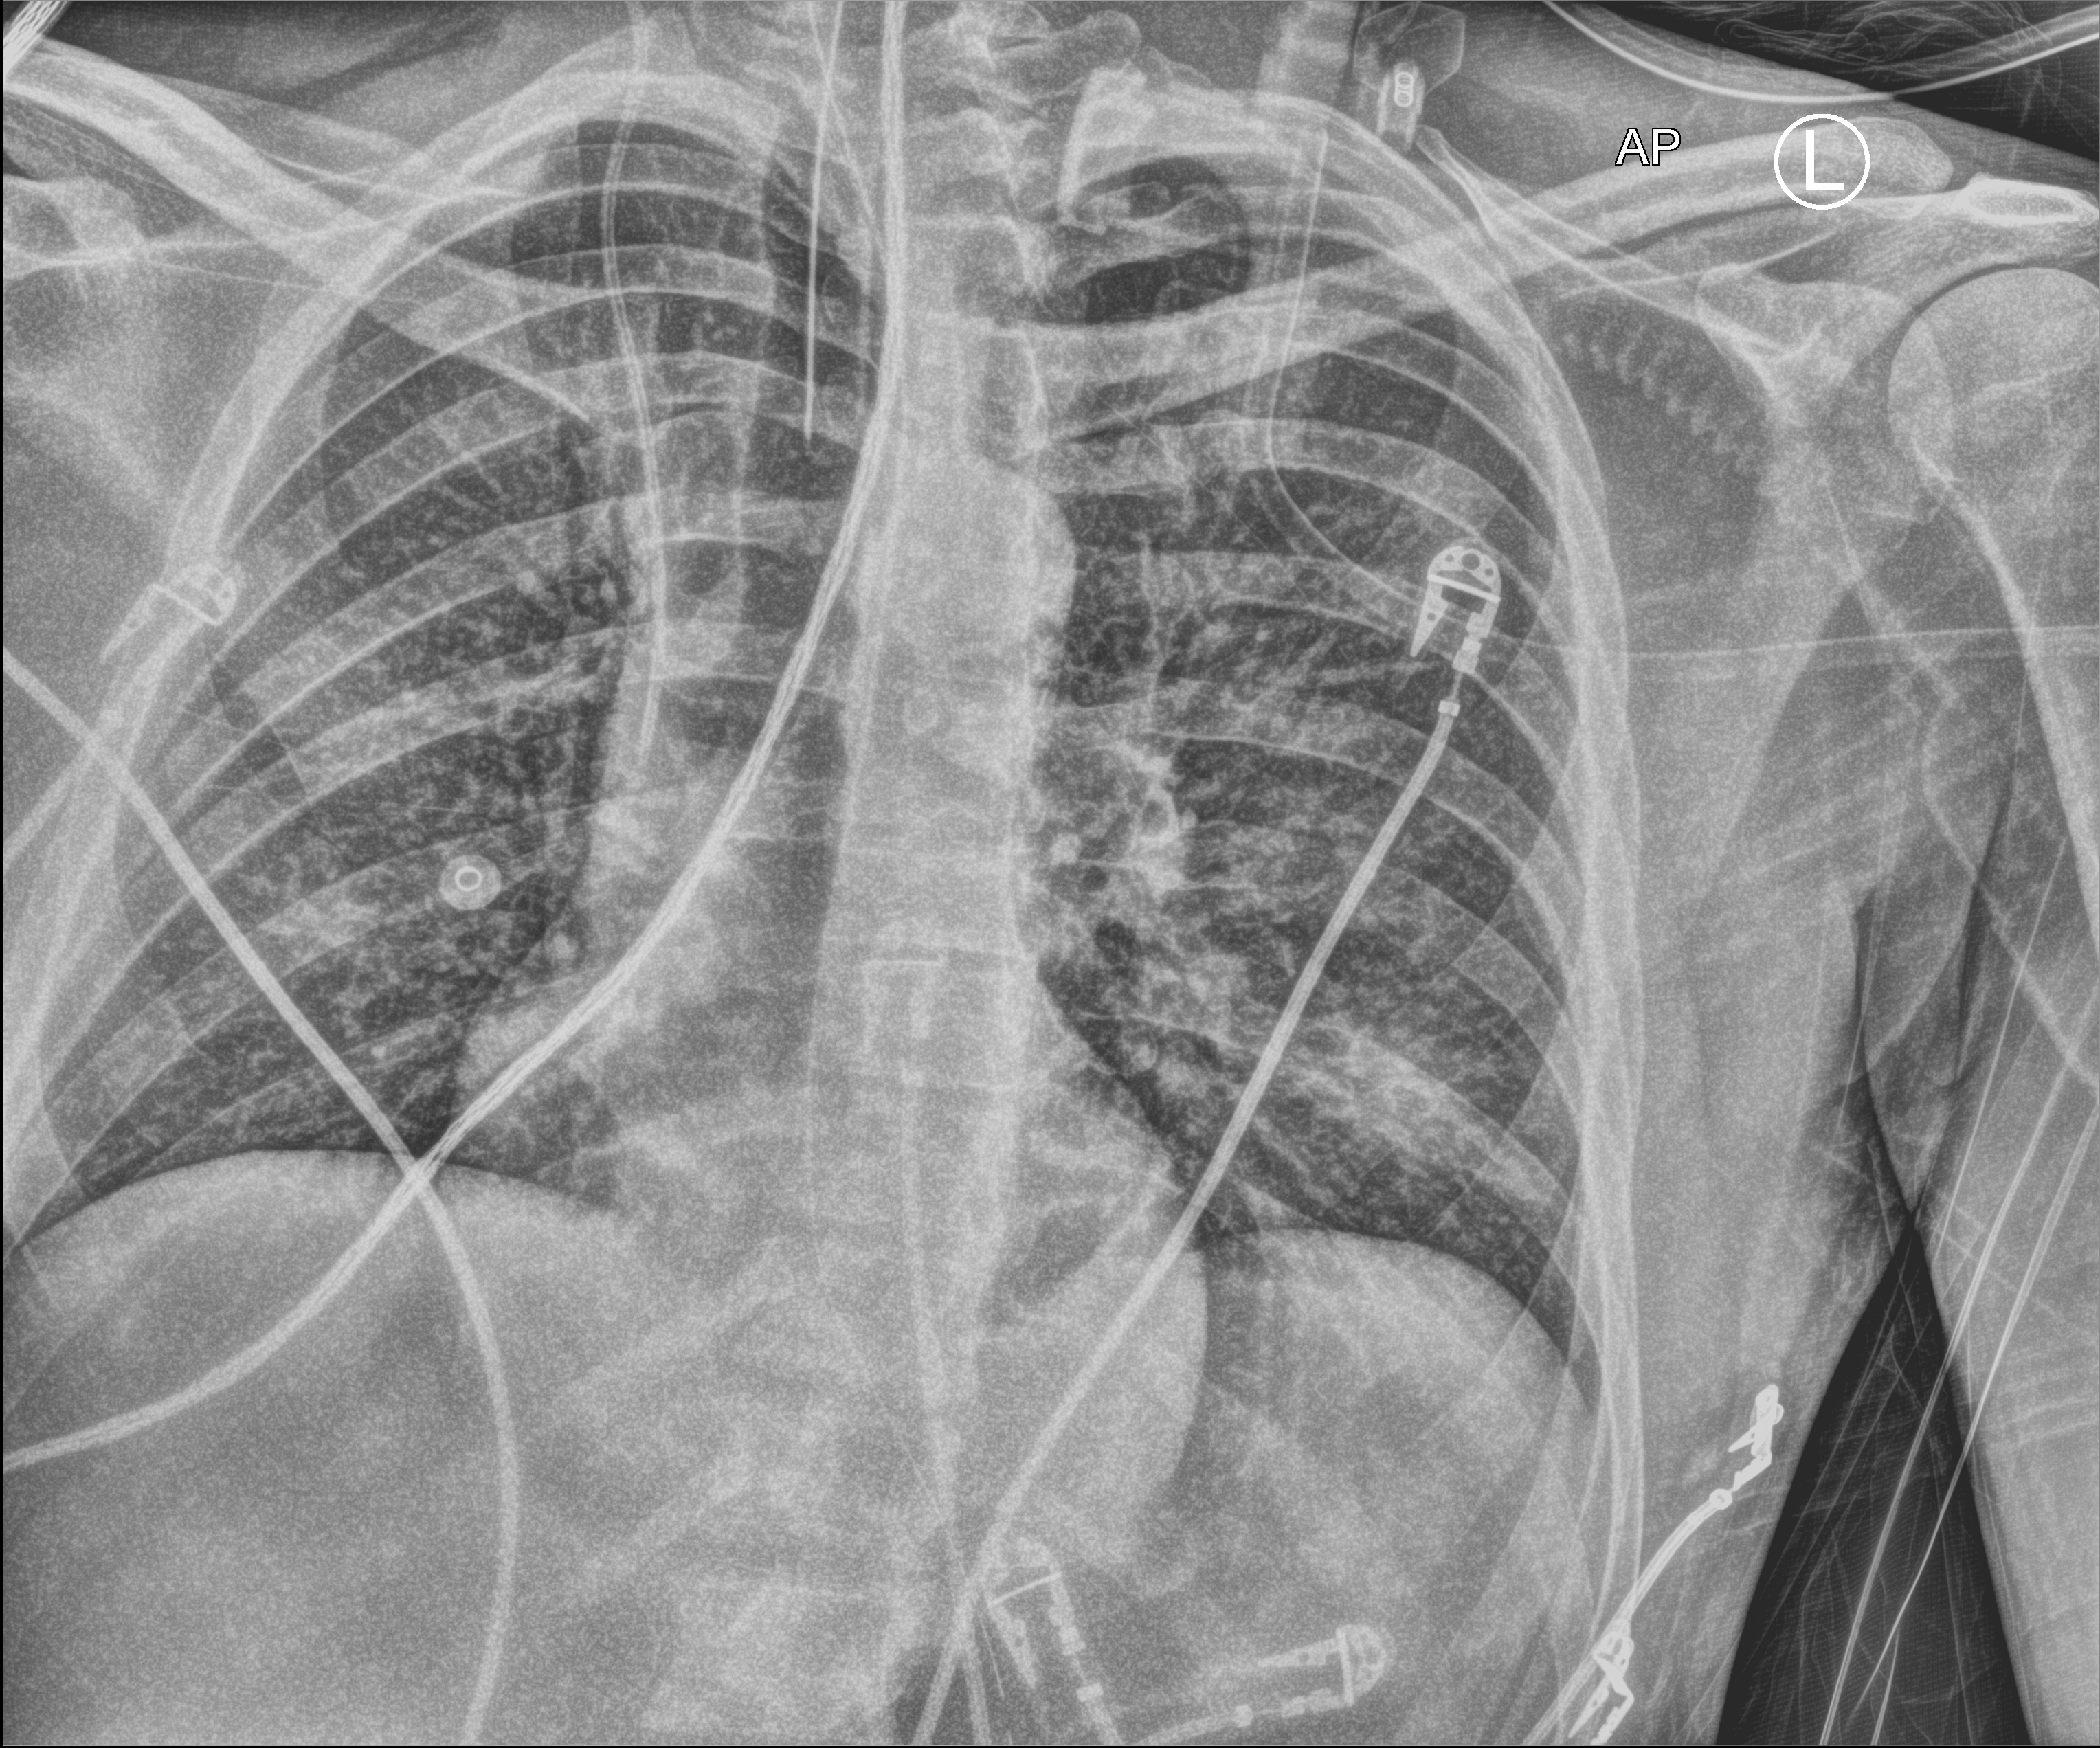
Bedside chest radiograph (computed radiography), anteroposterior (AP) projection. Male patient hospitalised with COVID-19, age 18–59 years.
Admission-level facts for this patient (not findings on this image; timing relative to this image not recorded):
- mechanically ventilated during this hospital stay: yes